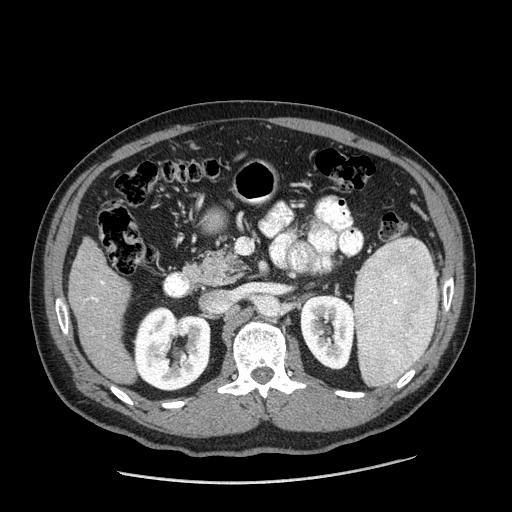
Contrast-enhanced abdominal CT (liver protocol), one axial slice. Slice 73 of 198 in the series (ordered by position). Reconstruction kernel STANDARD. 120 kVp. One of 2 acquisitions stored at this slice position. Soft-tissue window (W 400 / L 40 HU). 512 × 512 image matrix, field of view 400 × 400 mm. From the clinical record (not read from this slice): diagnosis: hepatocellular carcinoma (patient treated with transarterial chemoembolisation; whether this scan precedes or follows treatment is not stated here); TNM stage (as recorded): Stage-II; Child-Pugh class: A; tumour differentiation: moderately differentiated; tumour nodularity: multinodular.
Annotated regions visible in this slice (semi-automatically segmented with operator editing):
- liver parenchyma outside the tumour (the mass and vessels are separate outlines, so this box may not span the whole liver): bounding box <68,238,136,384> (left, top, right, bottom; pixels)
- liver vessels: <86,281,104,302>